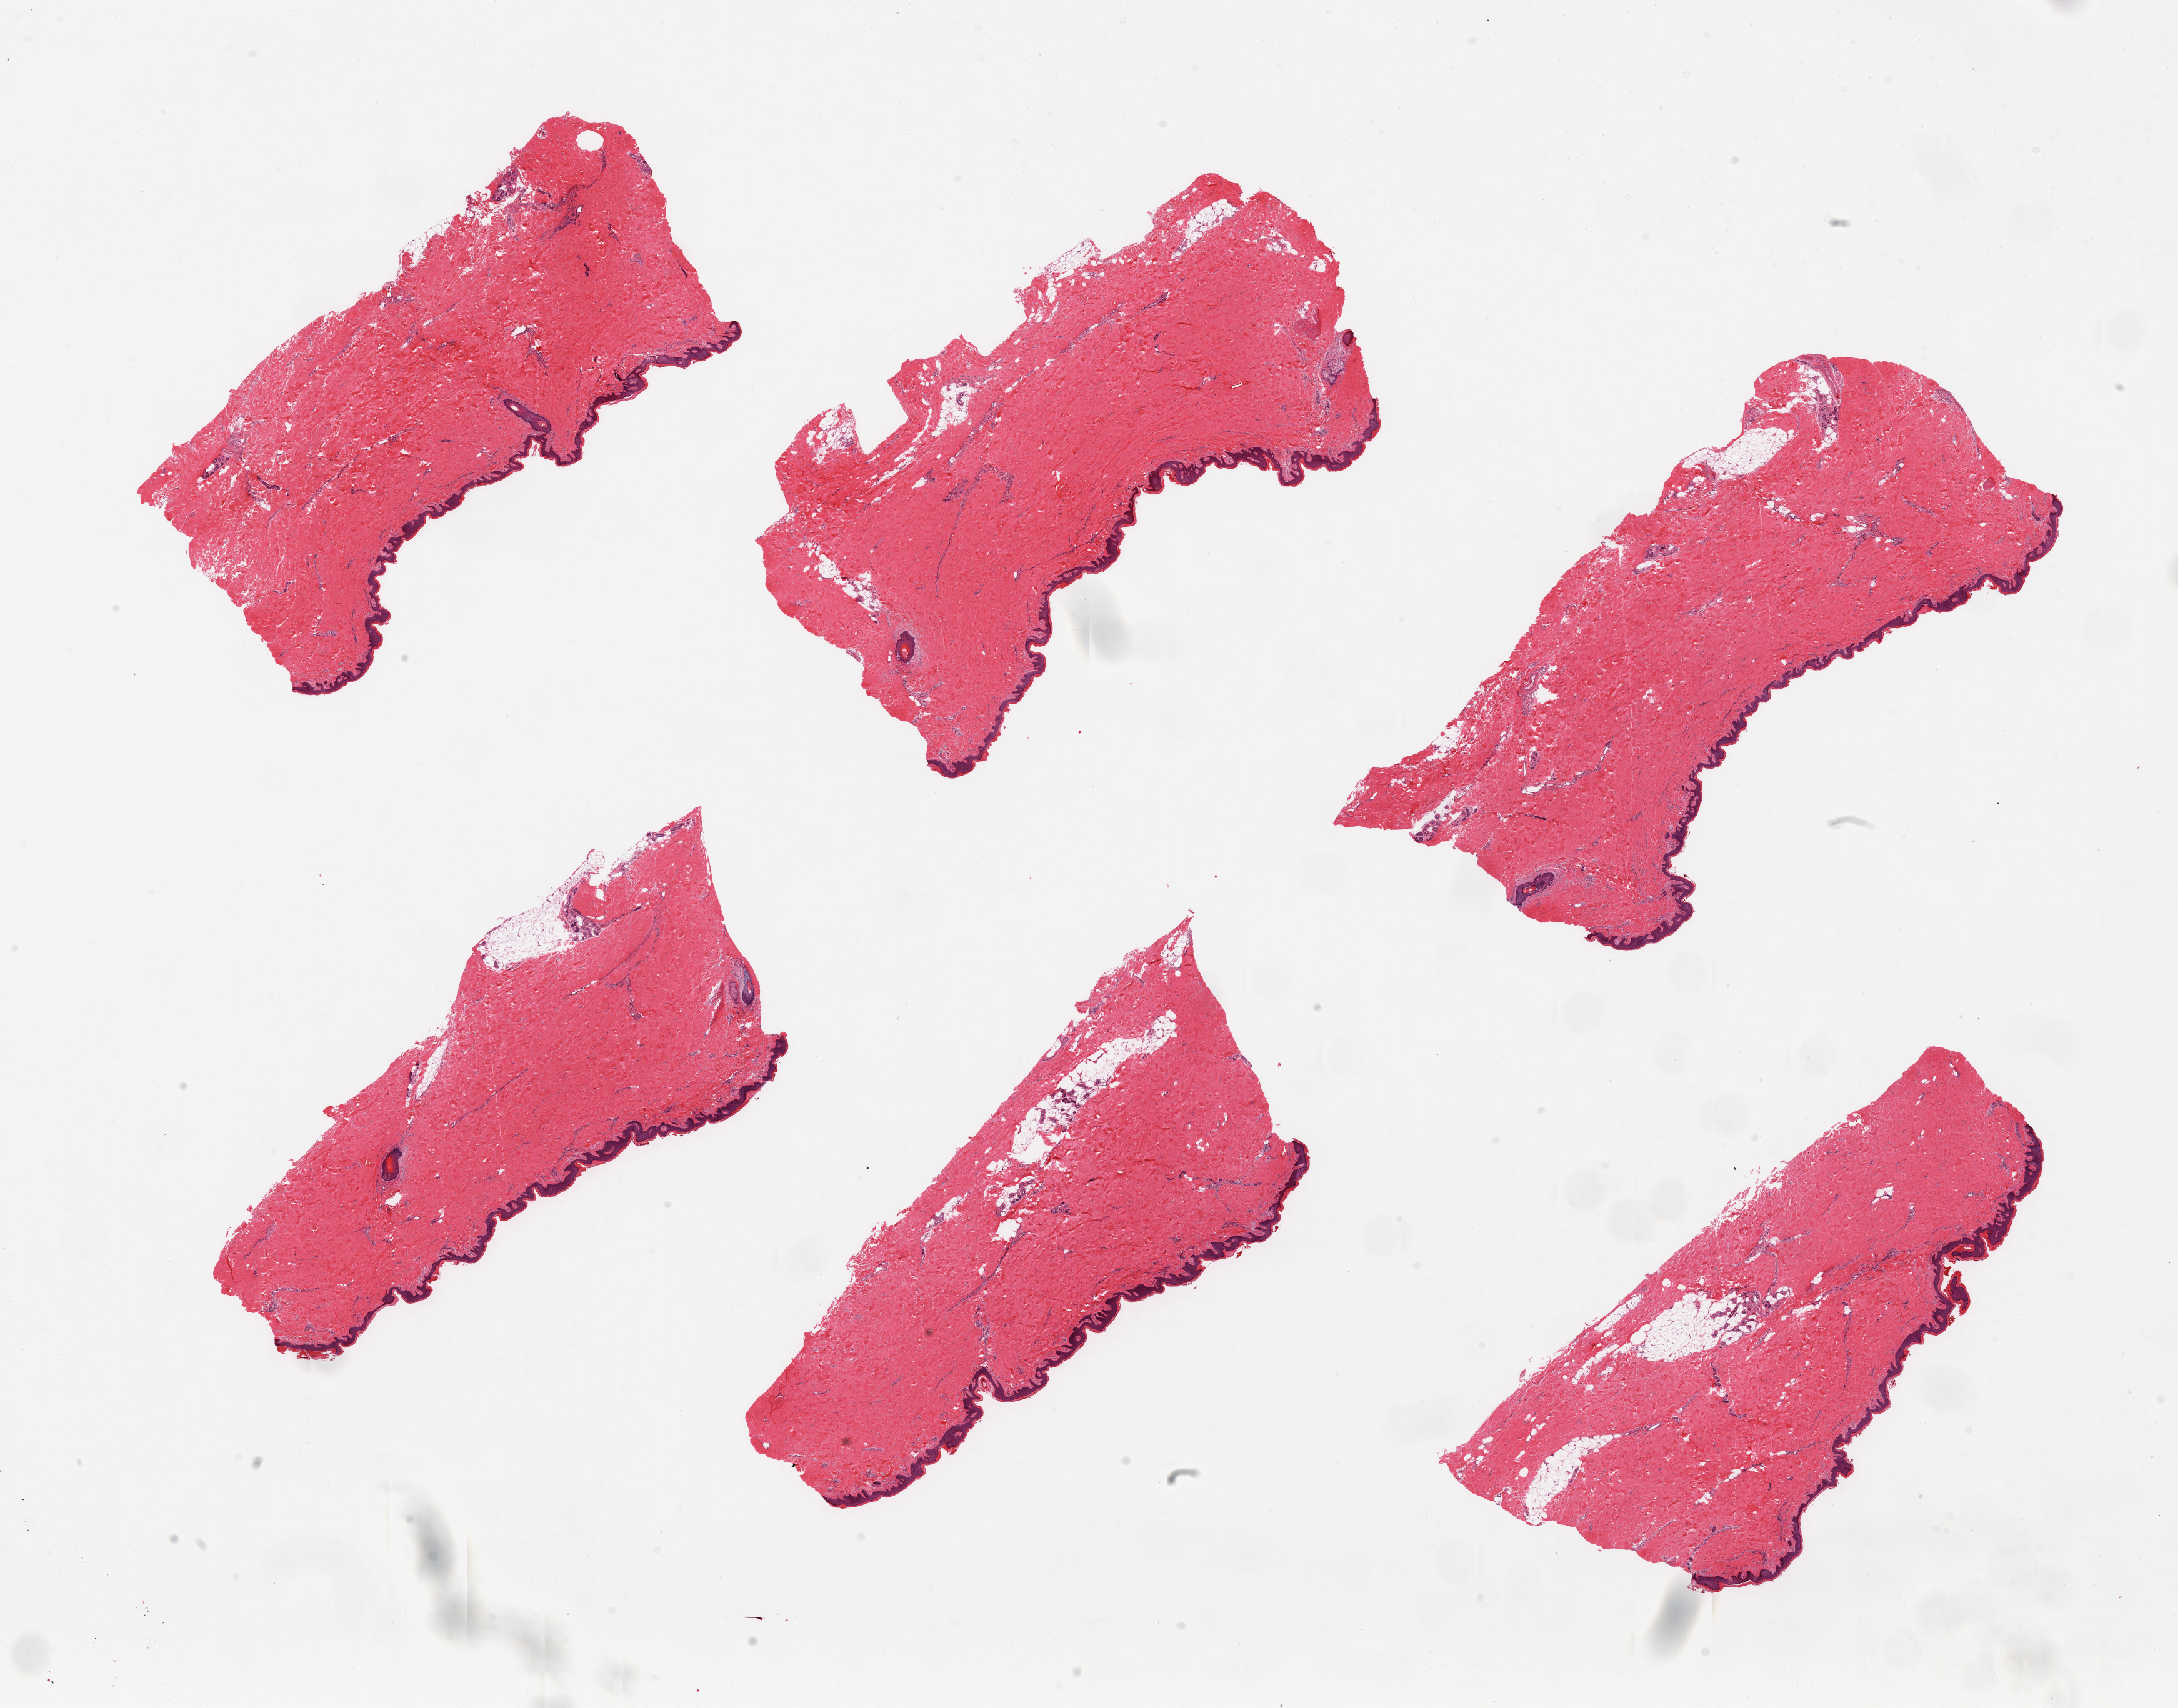
Digitized haematoxylin and eosin-stained section — whole scanned area (about 27.6 x 21.6 mm) shown as a low-resolution overview; PAXgene-fixed paraffin-embedded (PFPE) section; target tissue: skin of suprapubic region; donor tissue sample. Donor: male.
• review note (as recorded): 6 pieces, predominantly well trimmed with minimal internal and attached fat